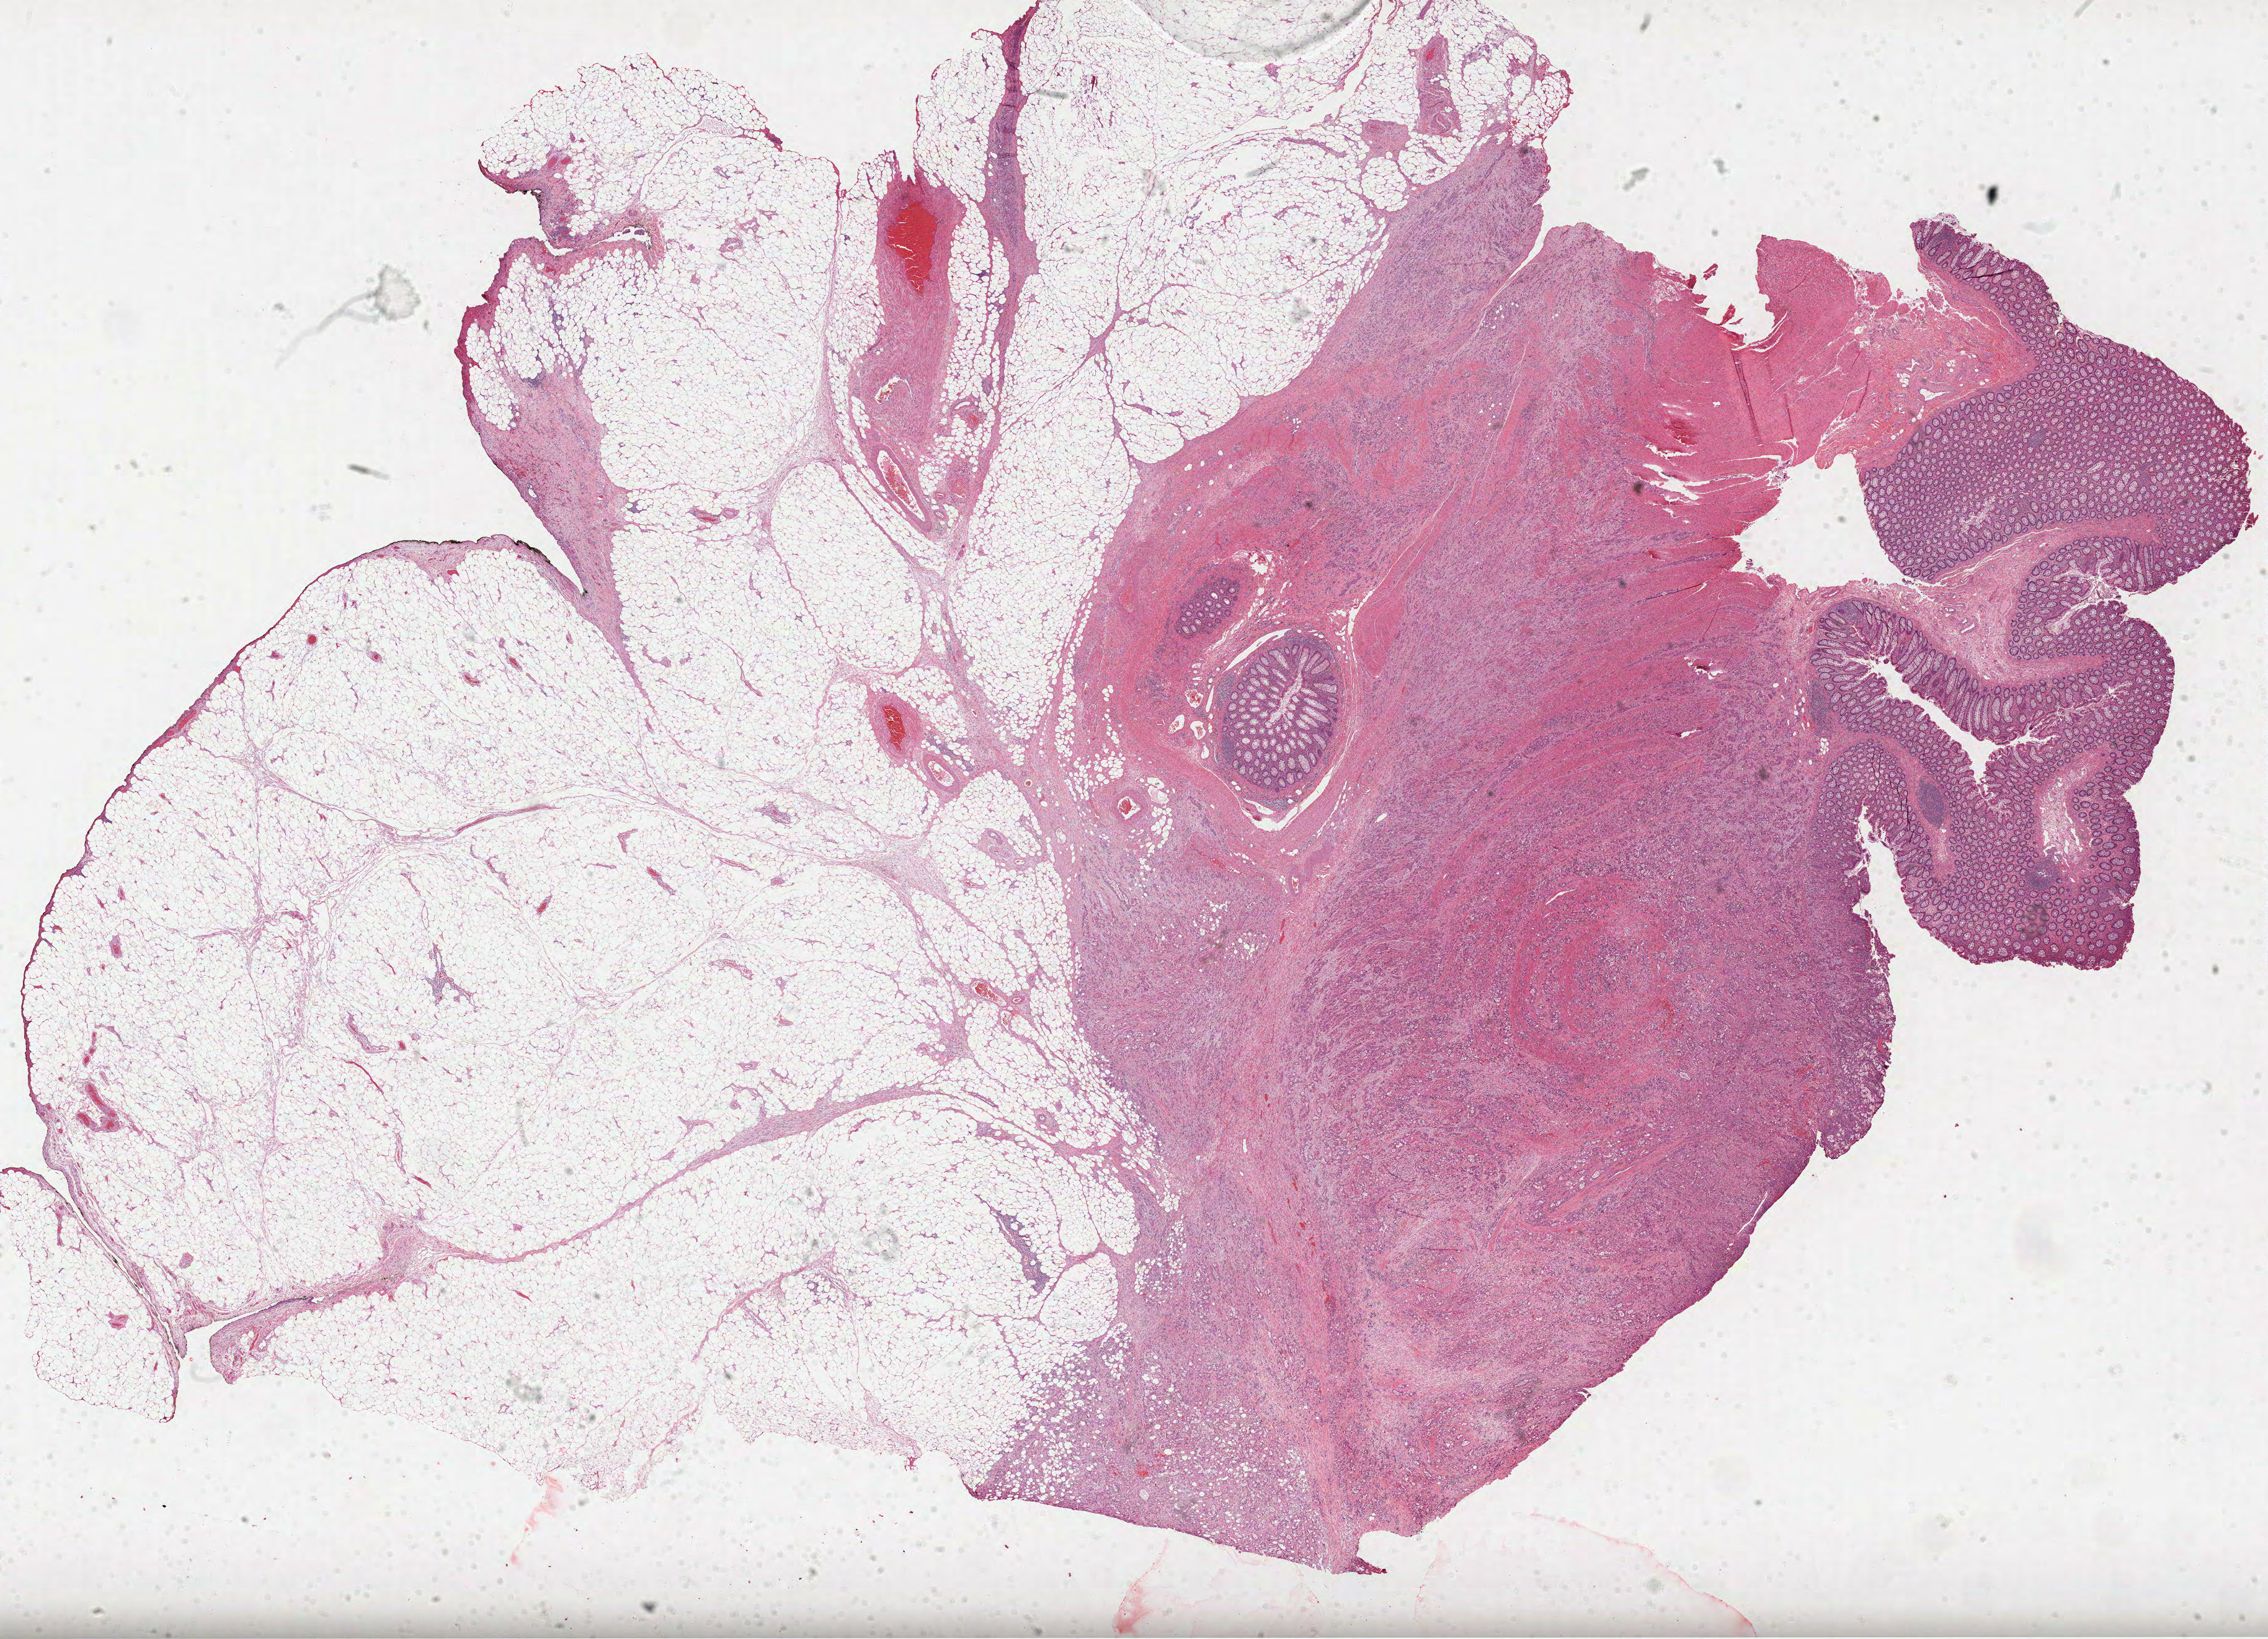
Digitized H&E tissue section (whole slide), shown as a low-resolution overview of the whole scanned area (about 29.5 x 21.3 mm, slide scanned at 40x). Formalin-fixed paraffin-embedded (FFPE) diagnostic section. Sample: primary tumour, colon. Male patient; age at initial diagnosis 69 years.
Lymph nodes positive (case pathology): 5 of 19 examined. Histologic diagnosis: Adenocarcinoma, NOS. AJCC pathologic stage: IV.